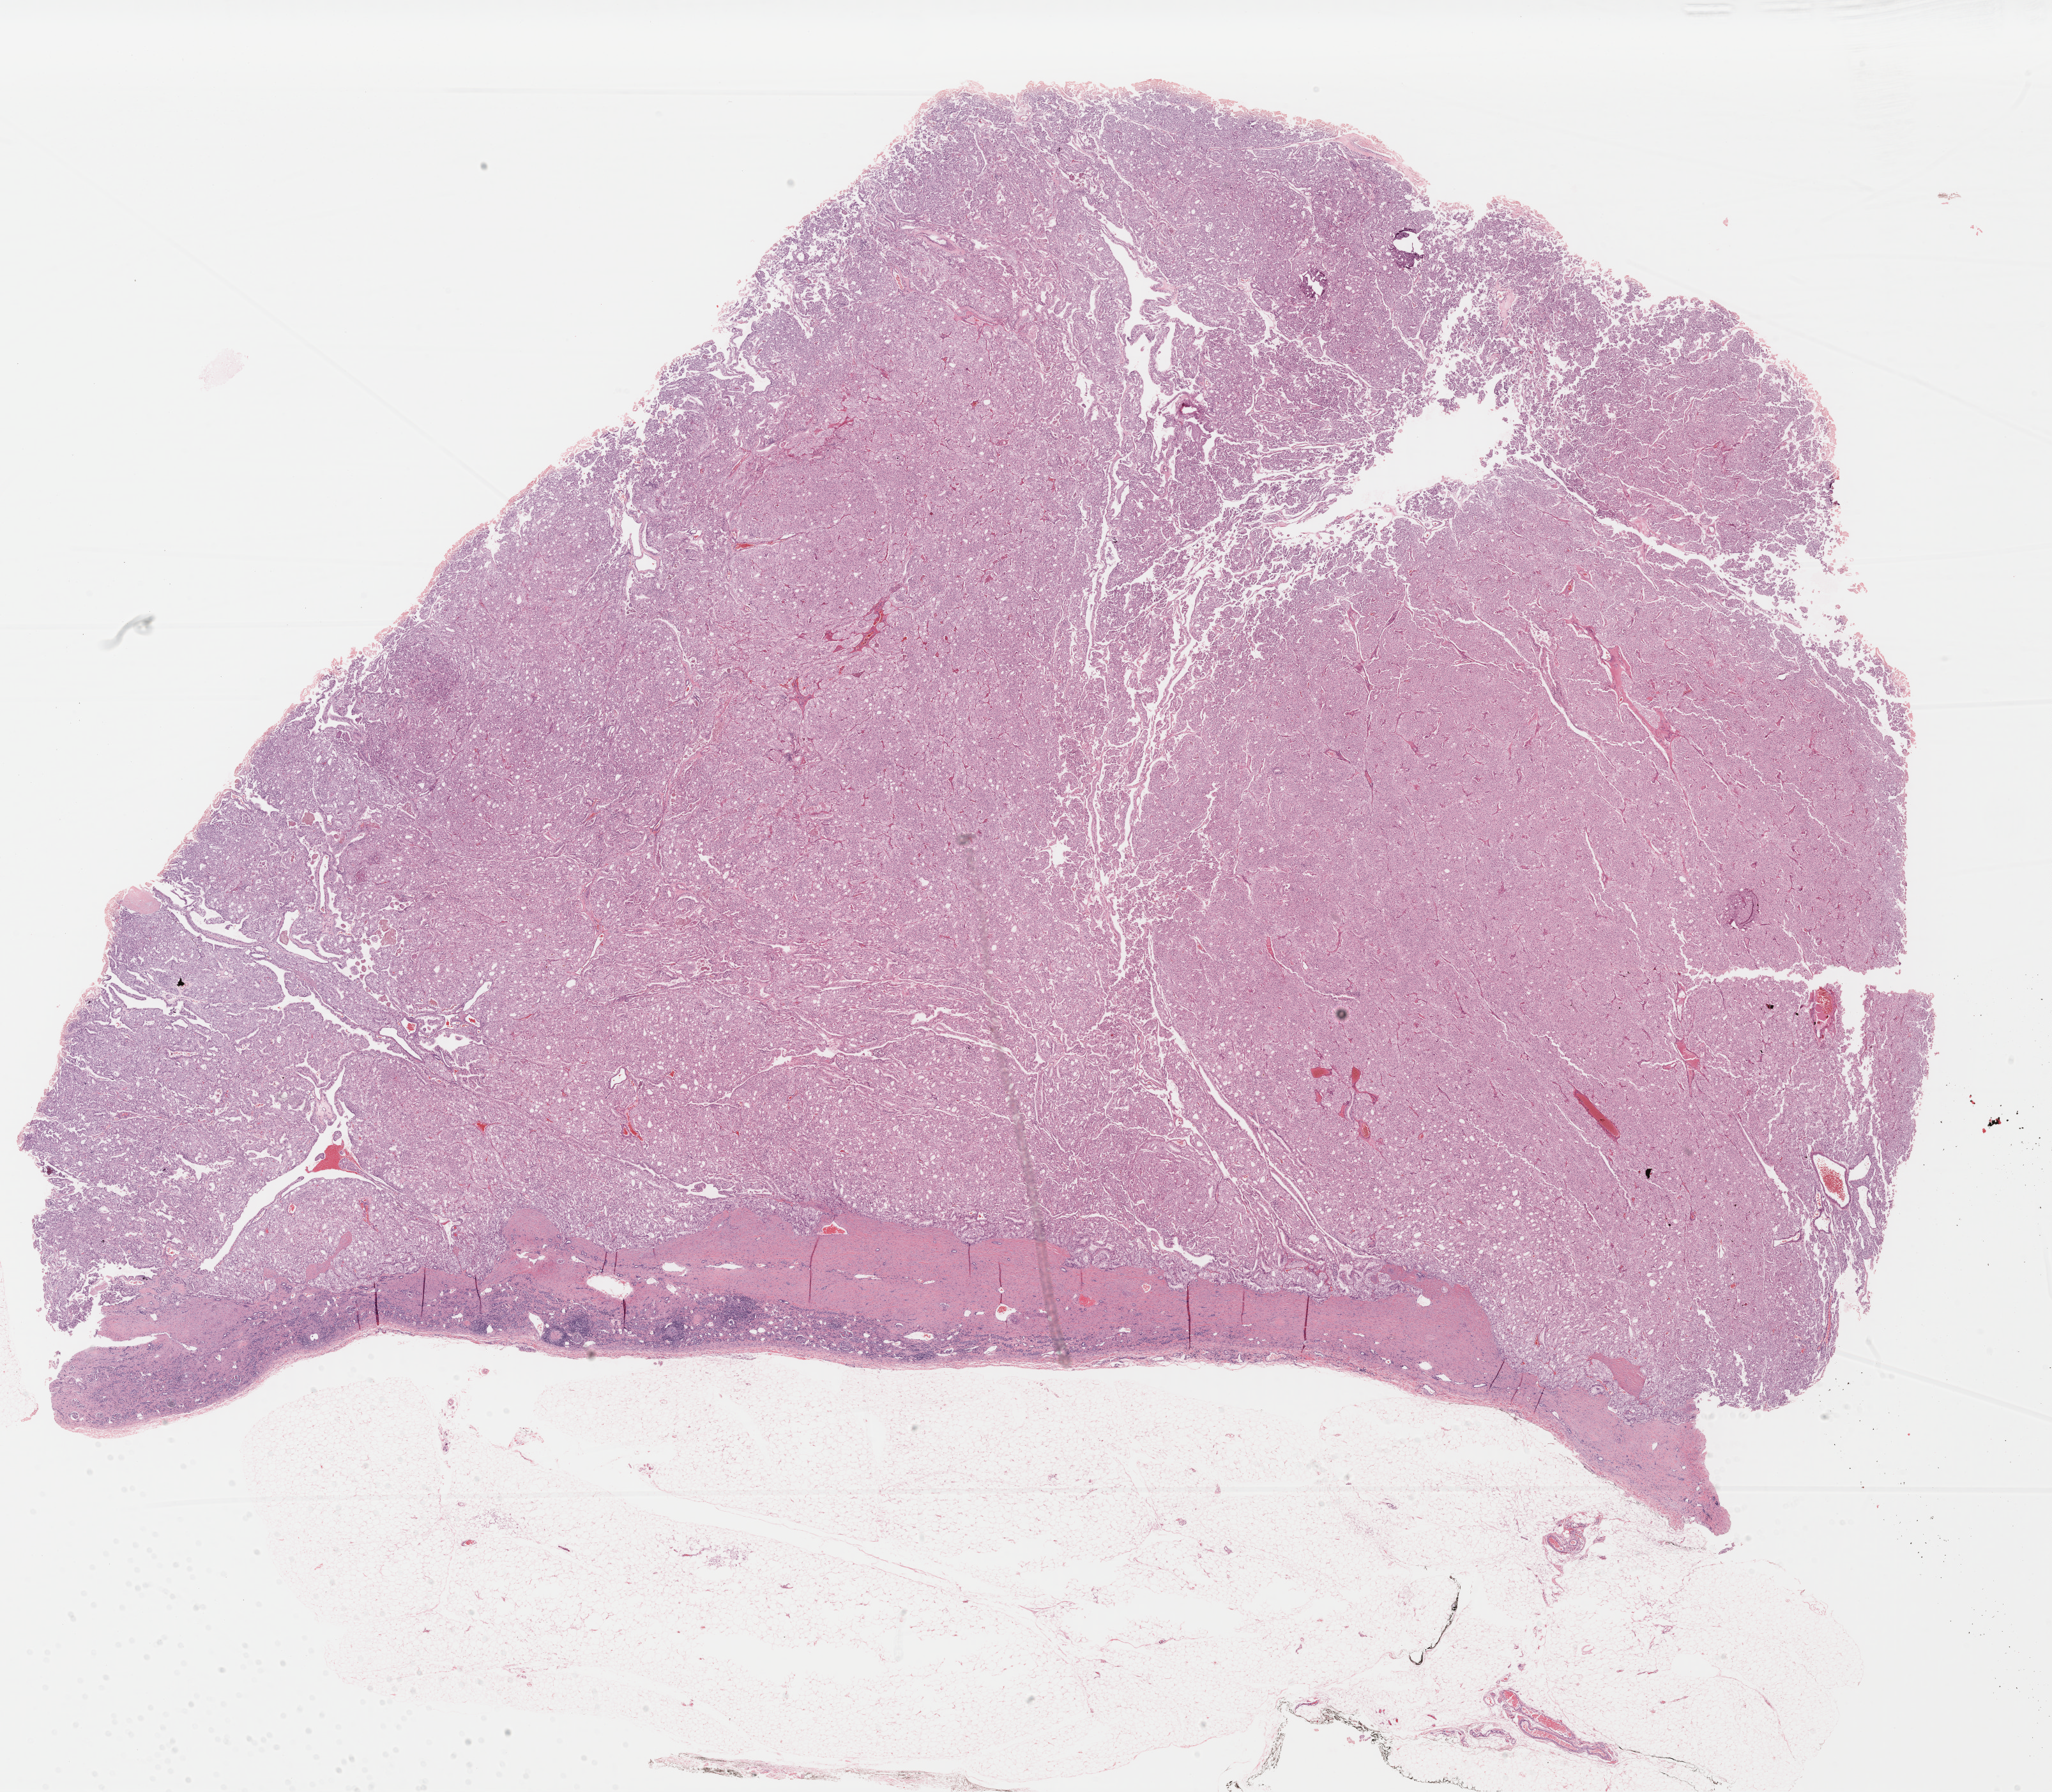
H&E-stained whole-slide image, a low-resolution overview of the entire scanned area, about 25.3 x 22.1 mm (acquisition: 40x scan). Formalin-fixed paraffin-embedded (FFPE) diagnostic section. Primary tumour sample from the kidney. Female patient; age at initial diagnosis 30 years.
Diagnosis: Renal cell carcinoma, chromophobe type. AJCC pathologic stage: I (7th edition).